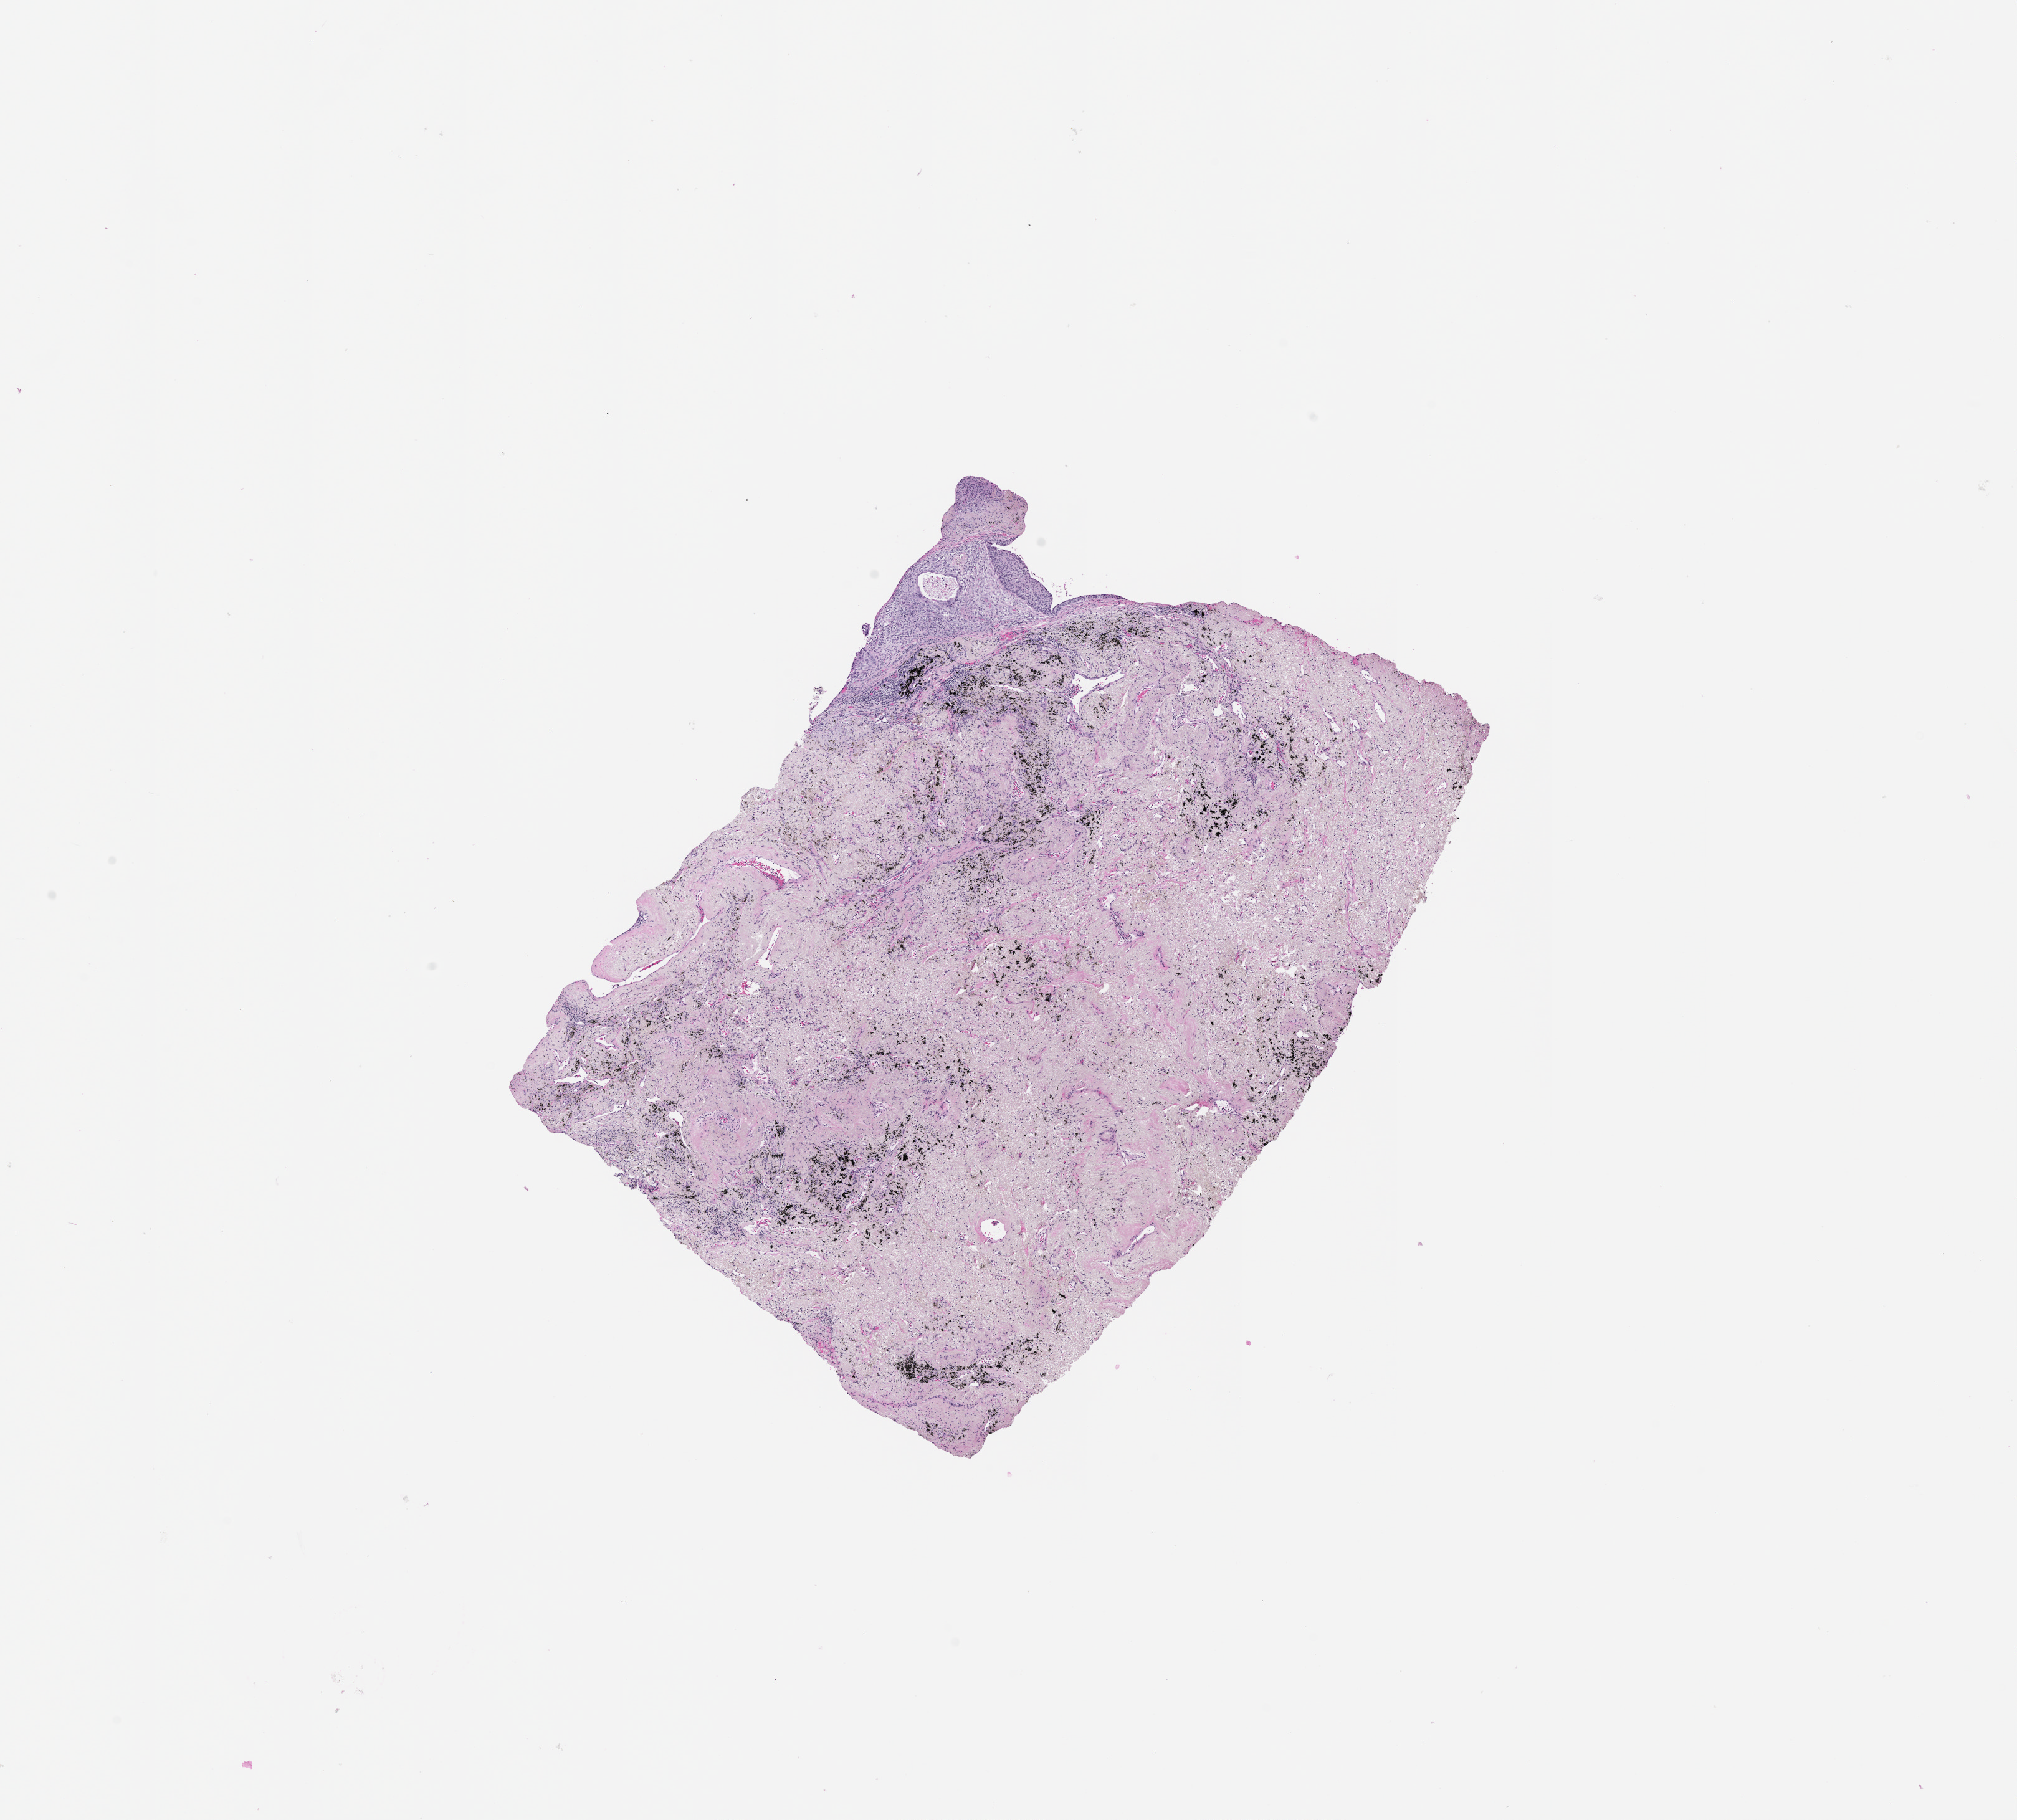
Whole-slide histology image, H&E-stained — whole scanned area (about 13.0 x 11.8 mm, from a 20x scan) shown as a low-resolution overview. Lung, tumour tissue. Female patient.
* patient diagnosis (cohort enrolment): squamous cell carcinoma (lung)